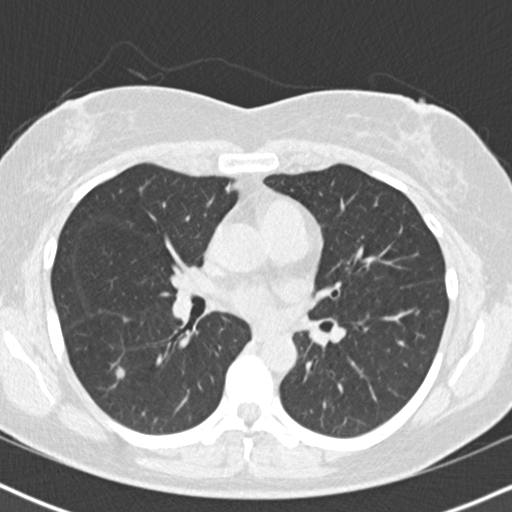
Axial slice from a low-dose chest CT screening exam; first (baseline) screen; lung window (W 1500 / L -600 HU); 2 mm slice thickness; 512 × 512 image matrix, field of view 320 × 320 mm. Female participant, aged 55 years at enrolment.
Lesion marked by an expert reader, bounding box <92,346,146,398> (left, top, right, bottom; pixels). The exam's reader record, not a measurement of the box and not confirmed to be the same lesion: non-calcified nodule or mass ≥4 mm, right lower lobe, 8 × 8 mm, poorly defined margins, soft tissue attenuation. Official screen result: positive, change unspecified: nodule(s) >= 4 mm or enlarging nodule(s), mass(es), or other non-specific abnormalities suspicious for lung cancer. Lung cancer was diagnosed 14 days after this screen: bronchiolo-alveolar adenocarcinoma, NOS, right lower lobe, well differentiated (G1), stage IA (AJCC 6th edition), 12 mm at pathology.